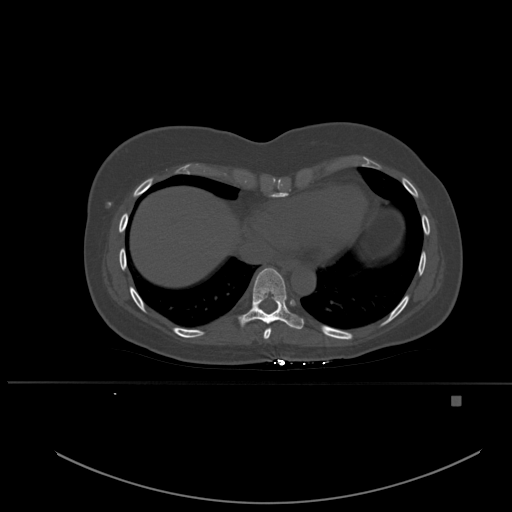
CT including the spine, one axial slice. Slice 307 of 651 in the series (ordered by position). Bone window (W 1800 / L 400 HU). 1.5 mm slice thickness. 512 × 512 image matrix, field of view 443 × 443 mm. Patient: female, 49 years. Case-level facts recorded for this patient, not image findings: primary cancer: breast; vertebrae with lytic lesions (as recorded): L3, T12, L4.
Structures marked on this image (semi-automatic segmentation, software-assisted and operator-edited):
- T8 vertebra: box from (x=263, y=329) to (x=271, y=339) px
- T9 vertebra: (x=238, y=268)–(x=304, y=331)